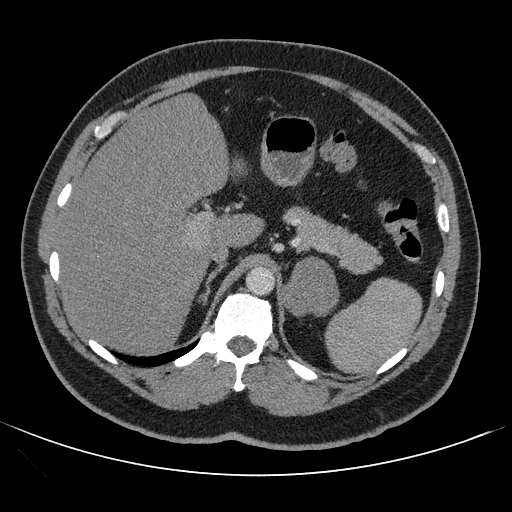
Contrast-enhanced abdominal CT, one axial slice. Position 75 of 121 along the scan axis. Intravenous contrast given. Soft-tissue window (W 400 / L 40 HU). 2.5 mm slice thickness. 512 × 512 image matrix. Male patient, age 53 years. Case-level facts recorded for this patient, not image findings: diagnosis: adrenocortical carcinoma; tumour side: left adrenal; tumour size at pathology: 7.9 cm; Ki-67 index: 20 %; stage (as recorded): 2.
Outlined on this slice (semi-automatic segmentation, software-assisted and operator-edited):
- mass: bounding box [x1, y1, x2, y2] px = [283, 257, 338, 316]